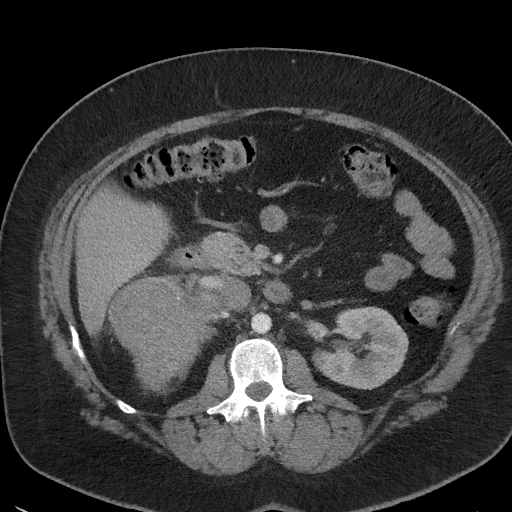
Contrast-enhanced abdominal CT, one axial slice. 120 kVp. Intravenous contrast given. Soft-tissue window (W 400 / L 40 HU). 512 × 512 image matrix, field of view 373 × 373 mm. Patient: female, 35 years. From the clinical record (not read from this slice): diagnosis: adrenocortical carcinoma; tumour side: right adrenal; tumour size at pathology: 15 cm; Ki-67 index: 40 %; stage (as recorded): 2.
Annotated regions visible in this slice (semi-automatic segmentation, software-assisted and operator-edited):
- mass: box from (x=111, y=280) to (x=220, y=390) px